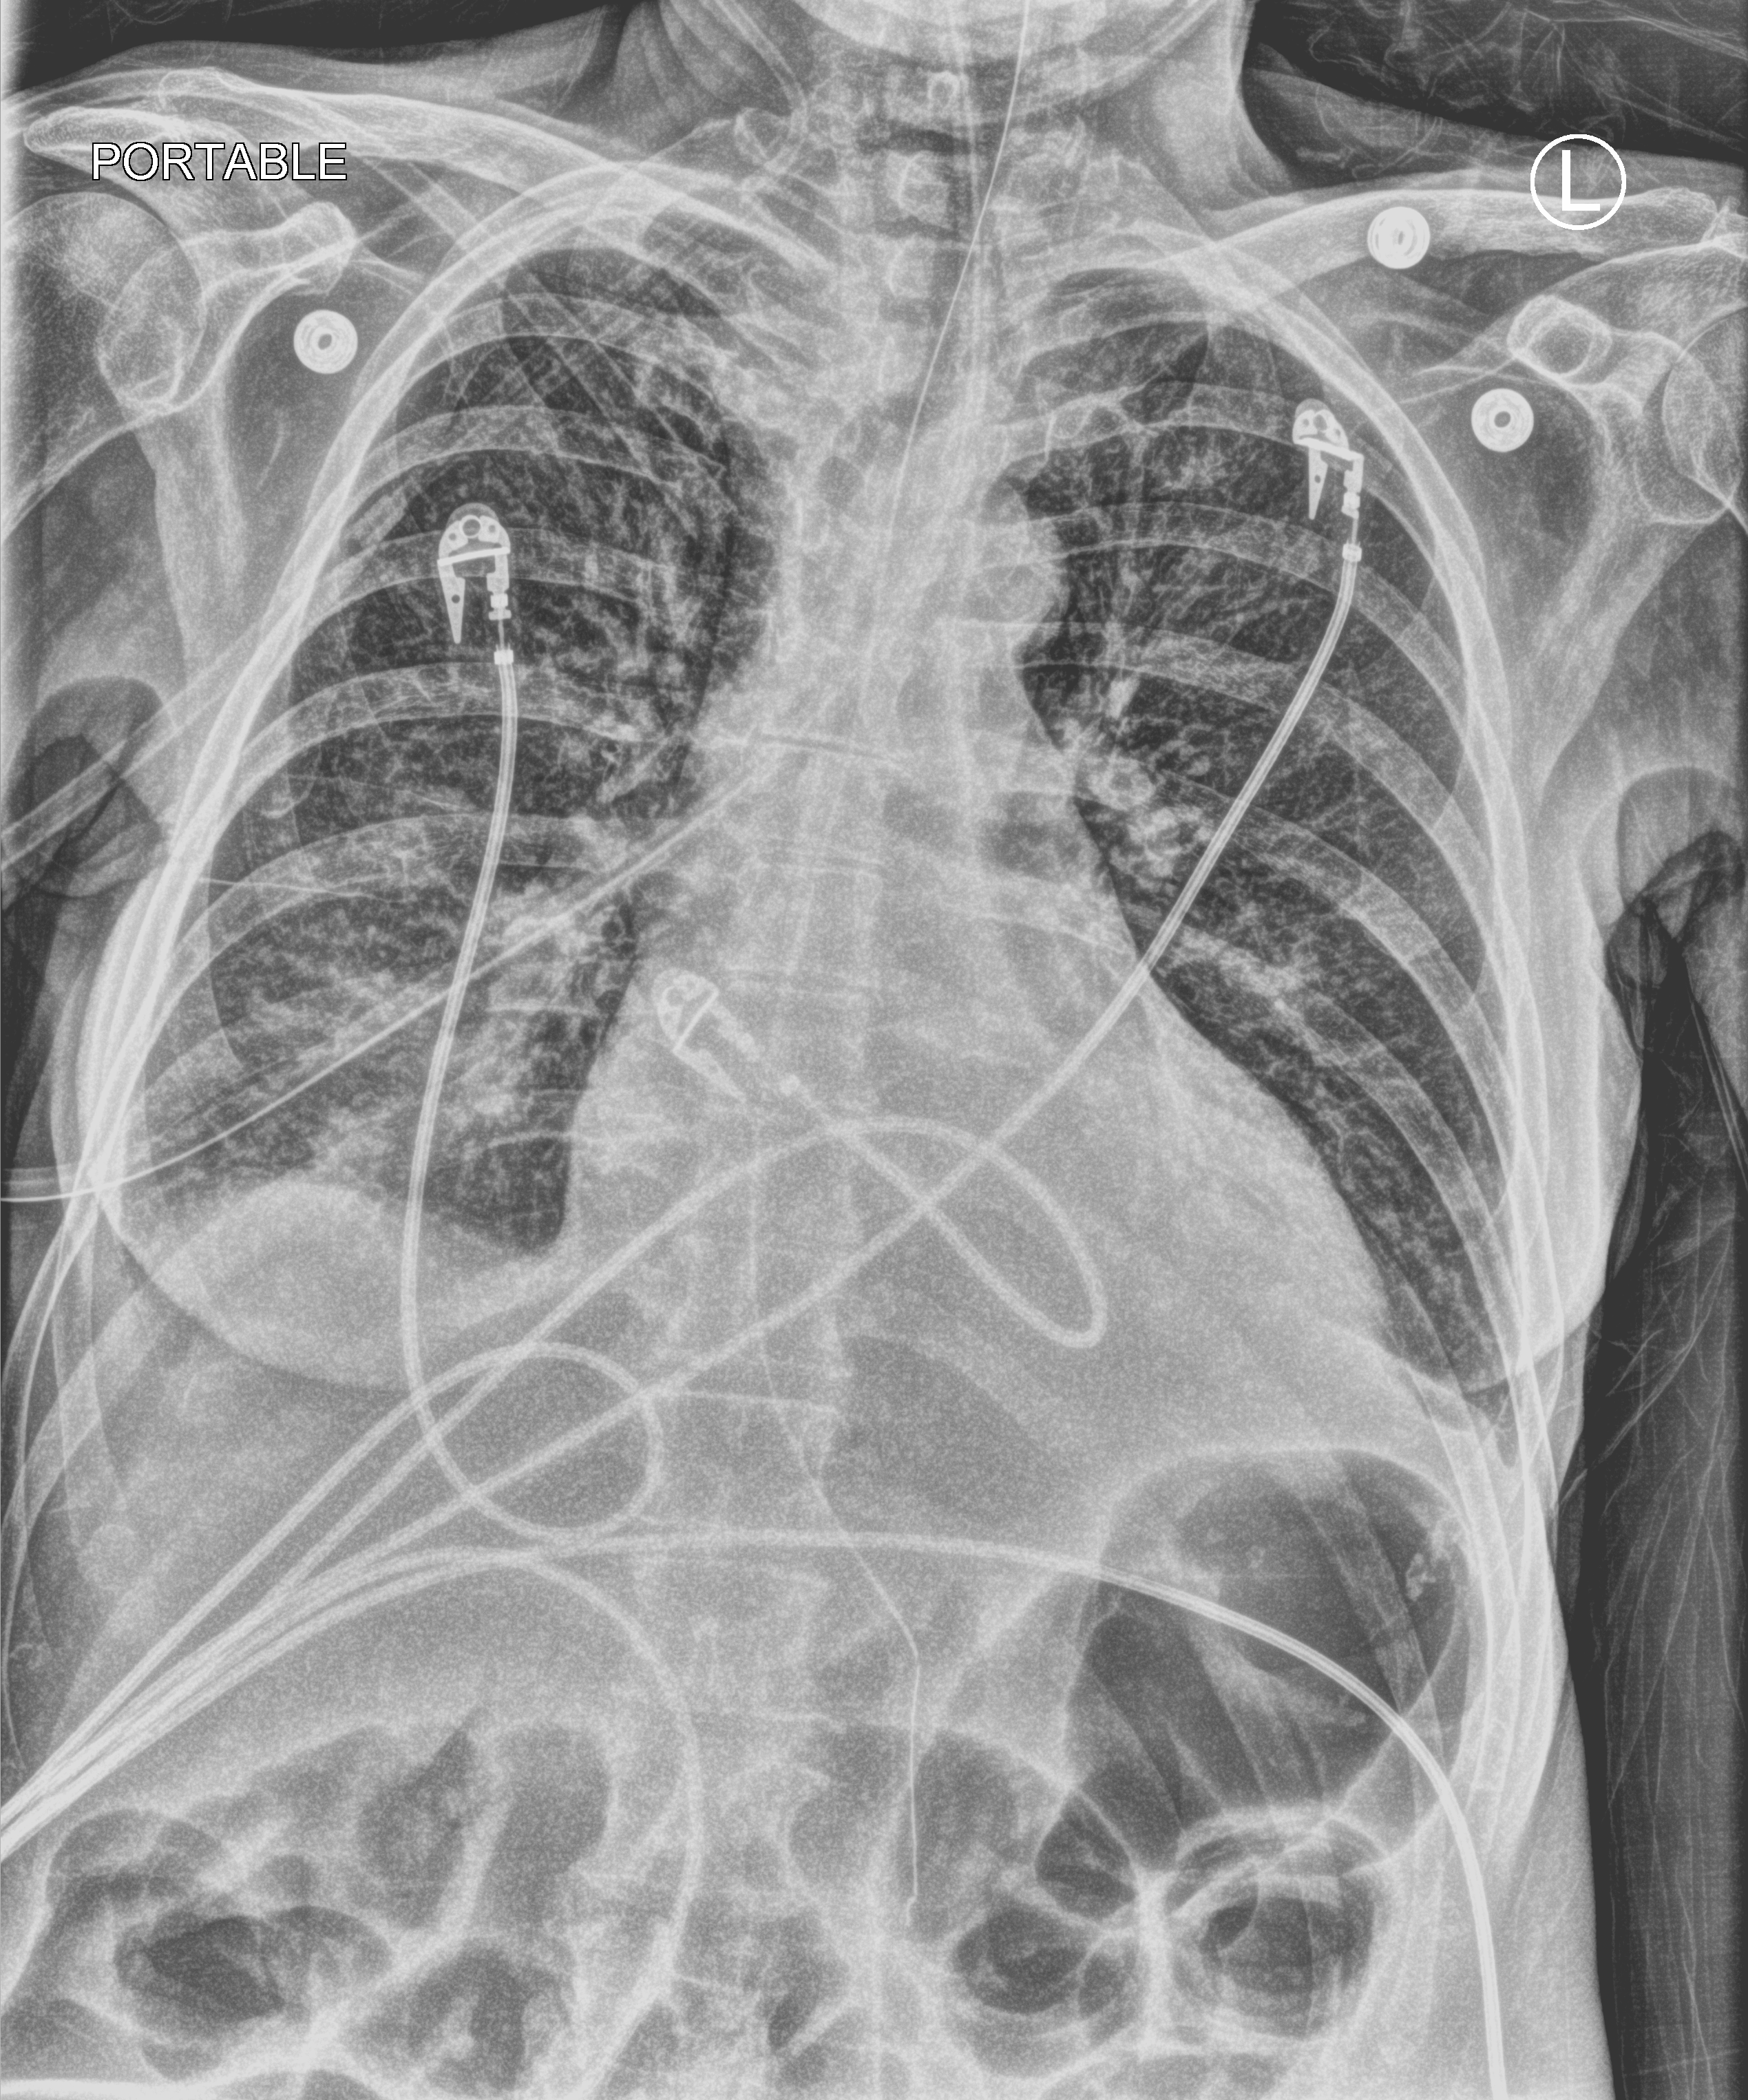
Bedside chest radiograph (computed radiography); anteroposterior (AP) projection. Female patient hospitalised with COVID-19, age 60–74 years.
From the hospital-stay record, not from the radiograph (when in the stay this image was taken is not recorded):
- mechanically ventilated during this hospital stay: yes